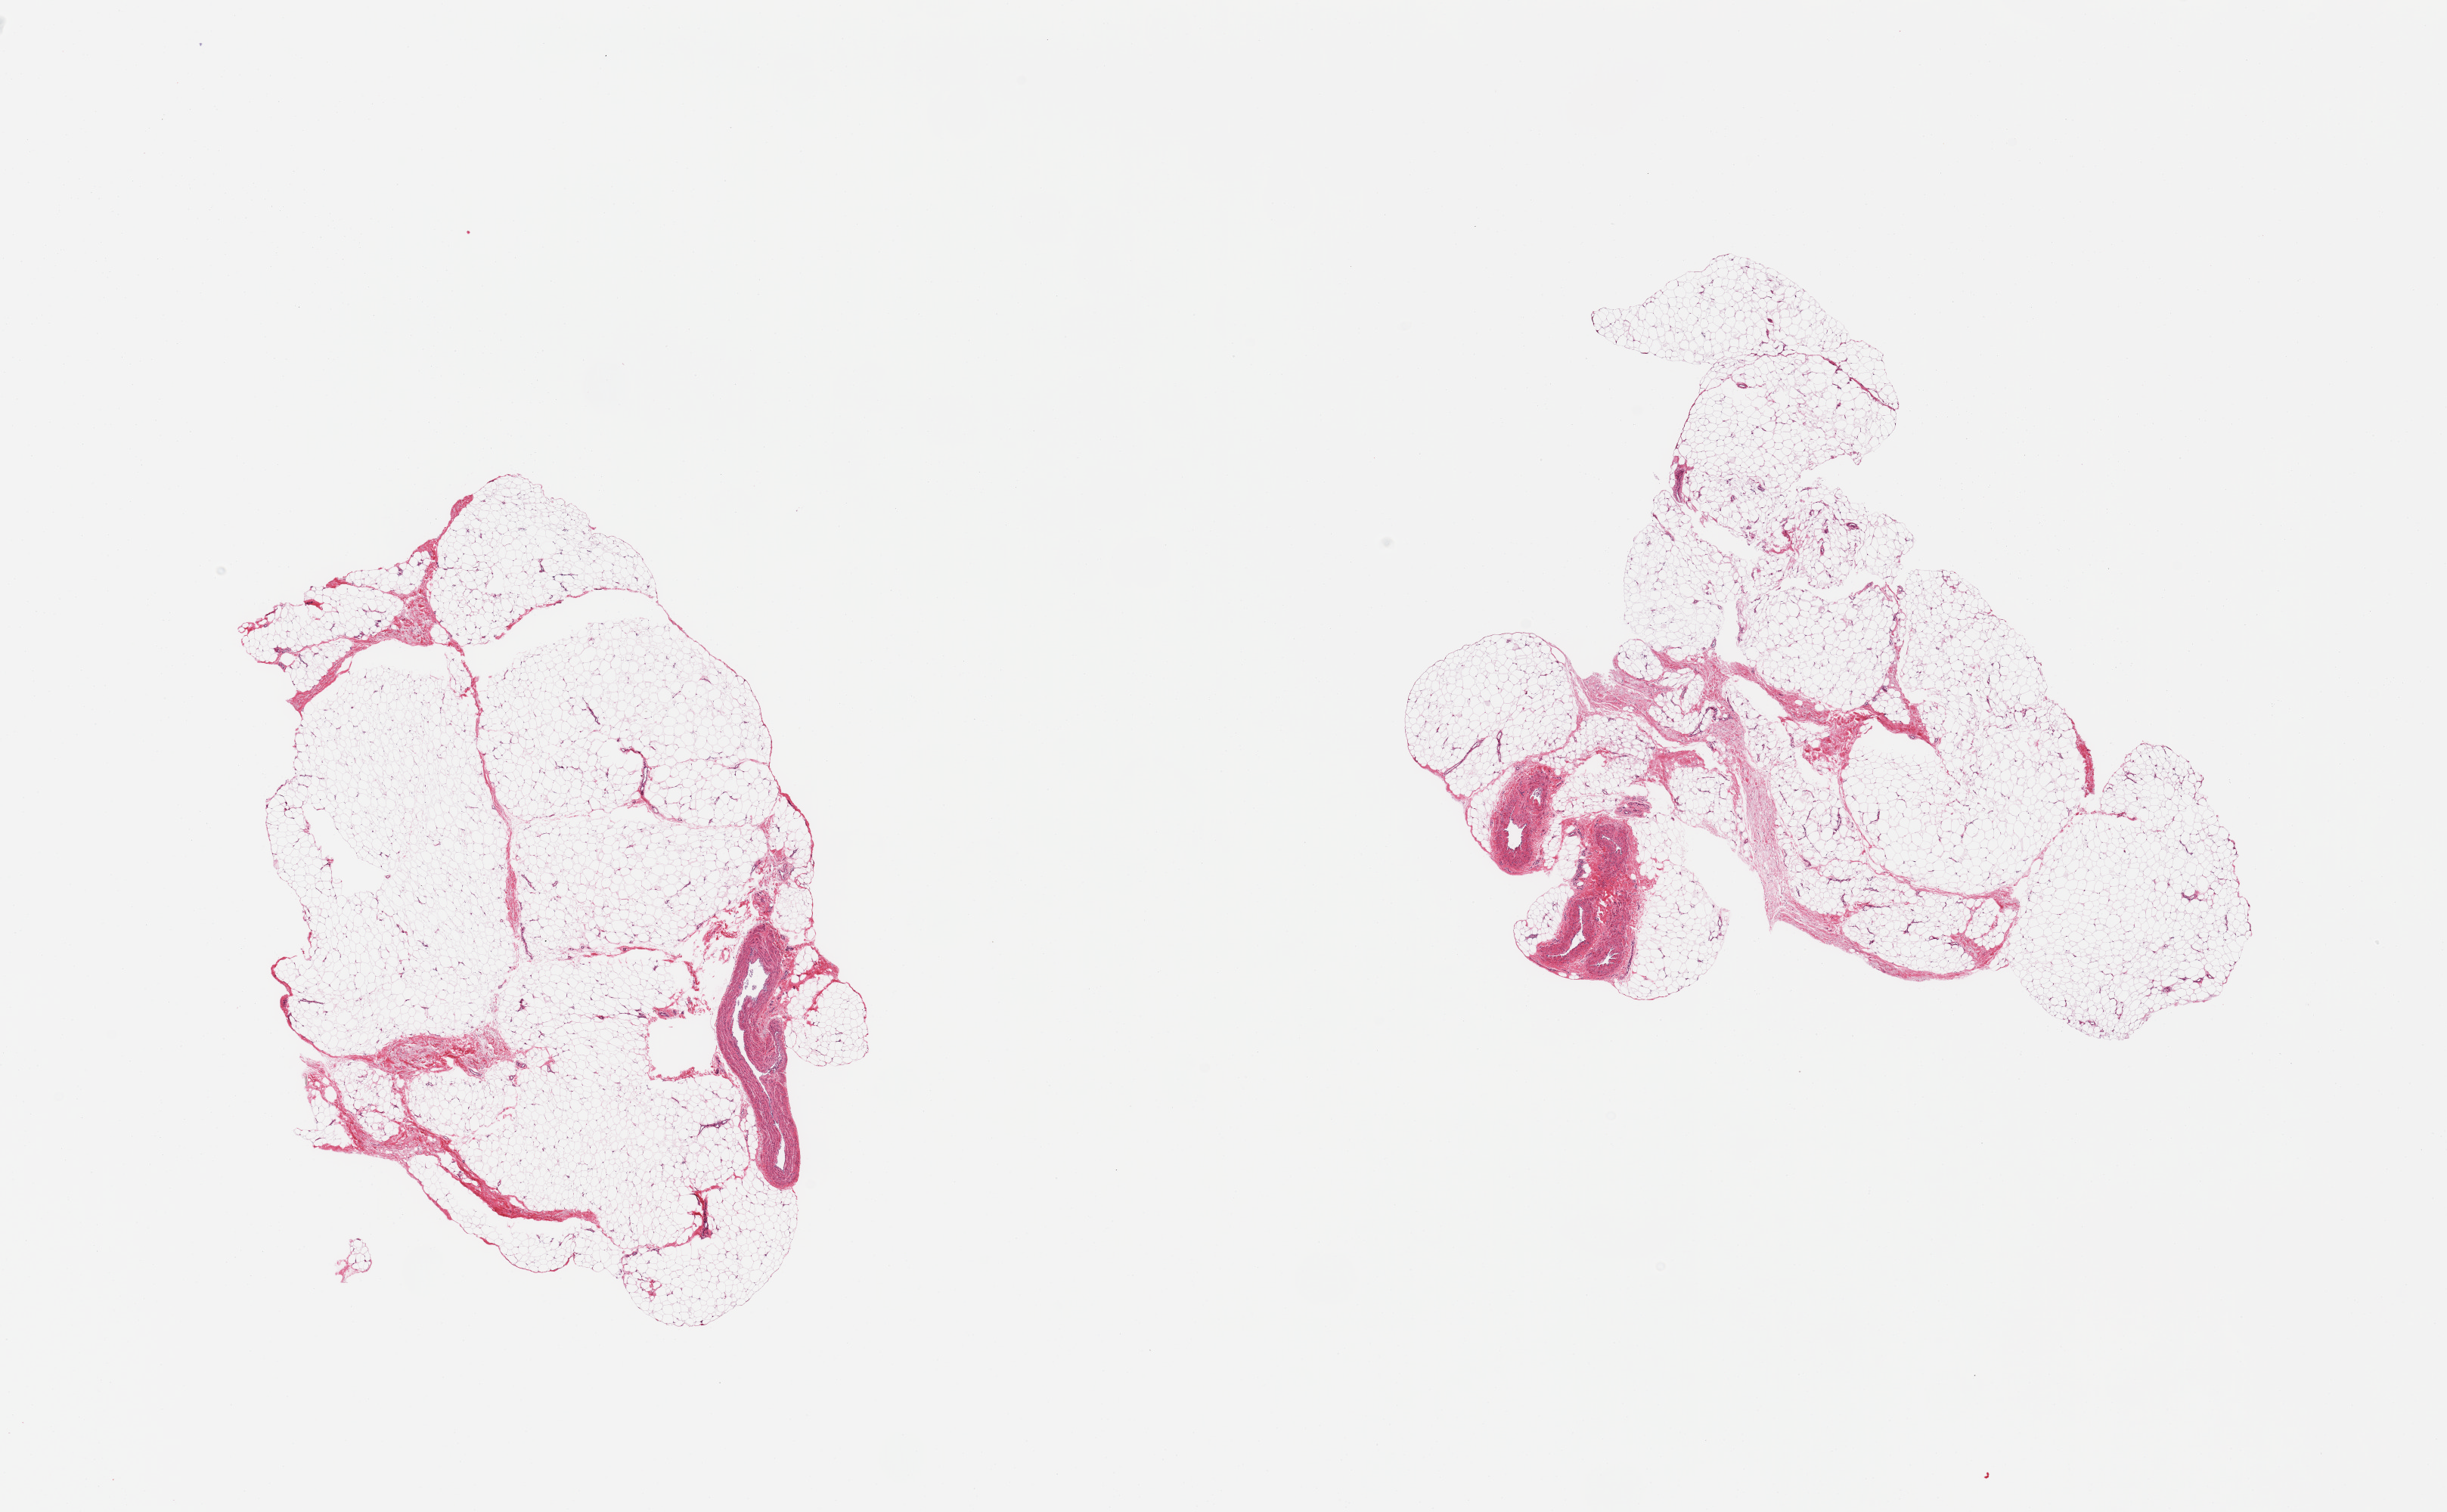
Digitized hematoxylin and eosin (H&E)-stained section, shown as a low-resolution overview of the whole scanned area (about 25.6 x 15.8 mm), PAXgene-fixed paraffin-embedded (PFPE) section, target tissue: adipose tissue, tissue donor sample. Male donor.
Pathologist's review note for this sample: 2 pieces, fascia/vascular elements ~10% of tissue.